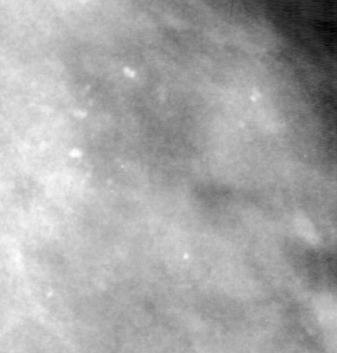
Cropped region of a digitized screen-film mammogram centred on a radiologist-marked abnormality, right breast, CC view, BI-RADS breast density category 4 (scale 1–4).
- Finding: calcifications, morphology pleomorphic, distribution clustered; BI-RADS assessment category 4; pathology result (as recorded, not read from the image): malignant.